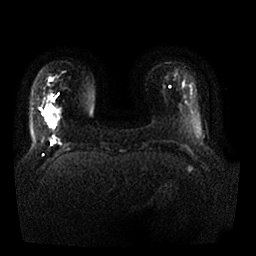
Breast MRI, one axial slice. Slice 5 of 25 in the series (ordered by position). Diffusion-weighted series; image 2 of 4 stored at this slice position (different b-values; order by instance number). 1.5 T. 4 mm slice thickness. 256 × 256 image matrix. Female patient.
Outlined on this slice (manually delineated by an expert):
- tumour on diffusion-weighted imaging: bounding box <46,106,60,128> (left, top, right, bottom; pixels)